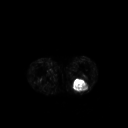
FDG PET of an extremity soft-tissue mass (from a PET/CT study), one axial slice; slice 192 of 267 in the series (ordered by position); 3.27 mm slice thickness; 128 × 128 image matrix, field of view 500 × 500 mm. Patient: male, 54 years. Case-level facts recorded for this patient, not image findings: histological type: synovial sarcoma; site of the primary tumour: left poplietal fossa.
Annotated regions visible in this slice (expert contour drawn on MRI and transferred to this co-registered scan by the dataset authors):
- gross tumour volume (mass): bounding box [x1, y1, x2, y2] px = [72, 79, 90, 93]